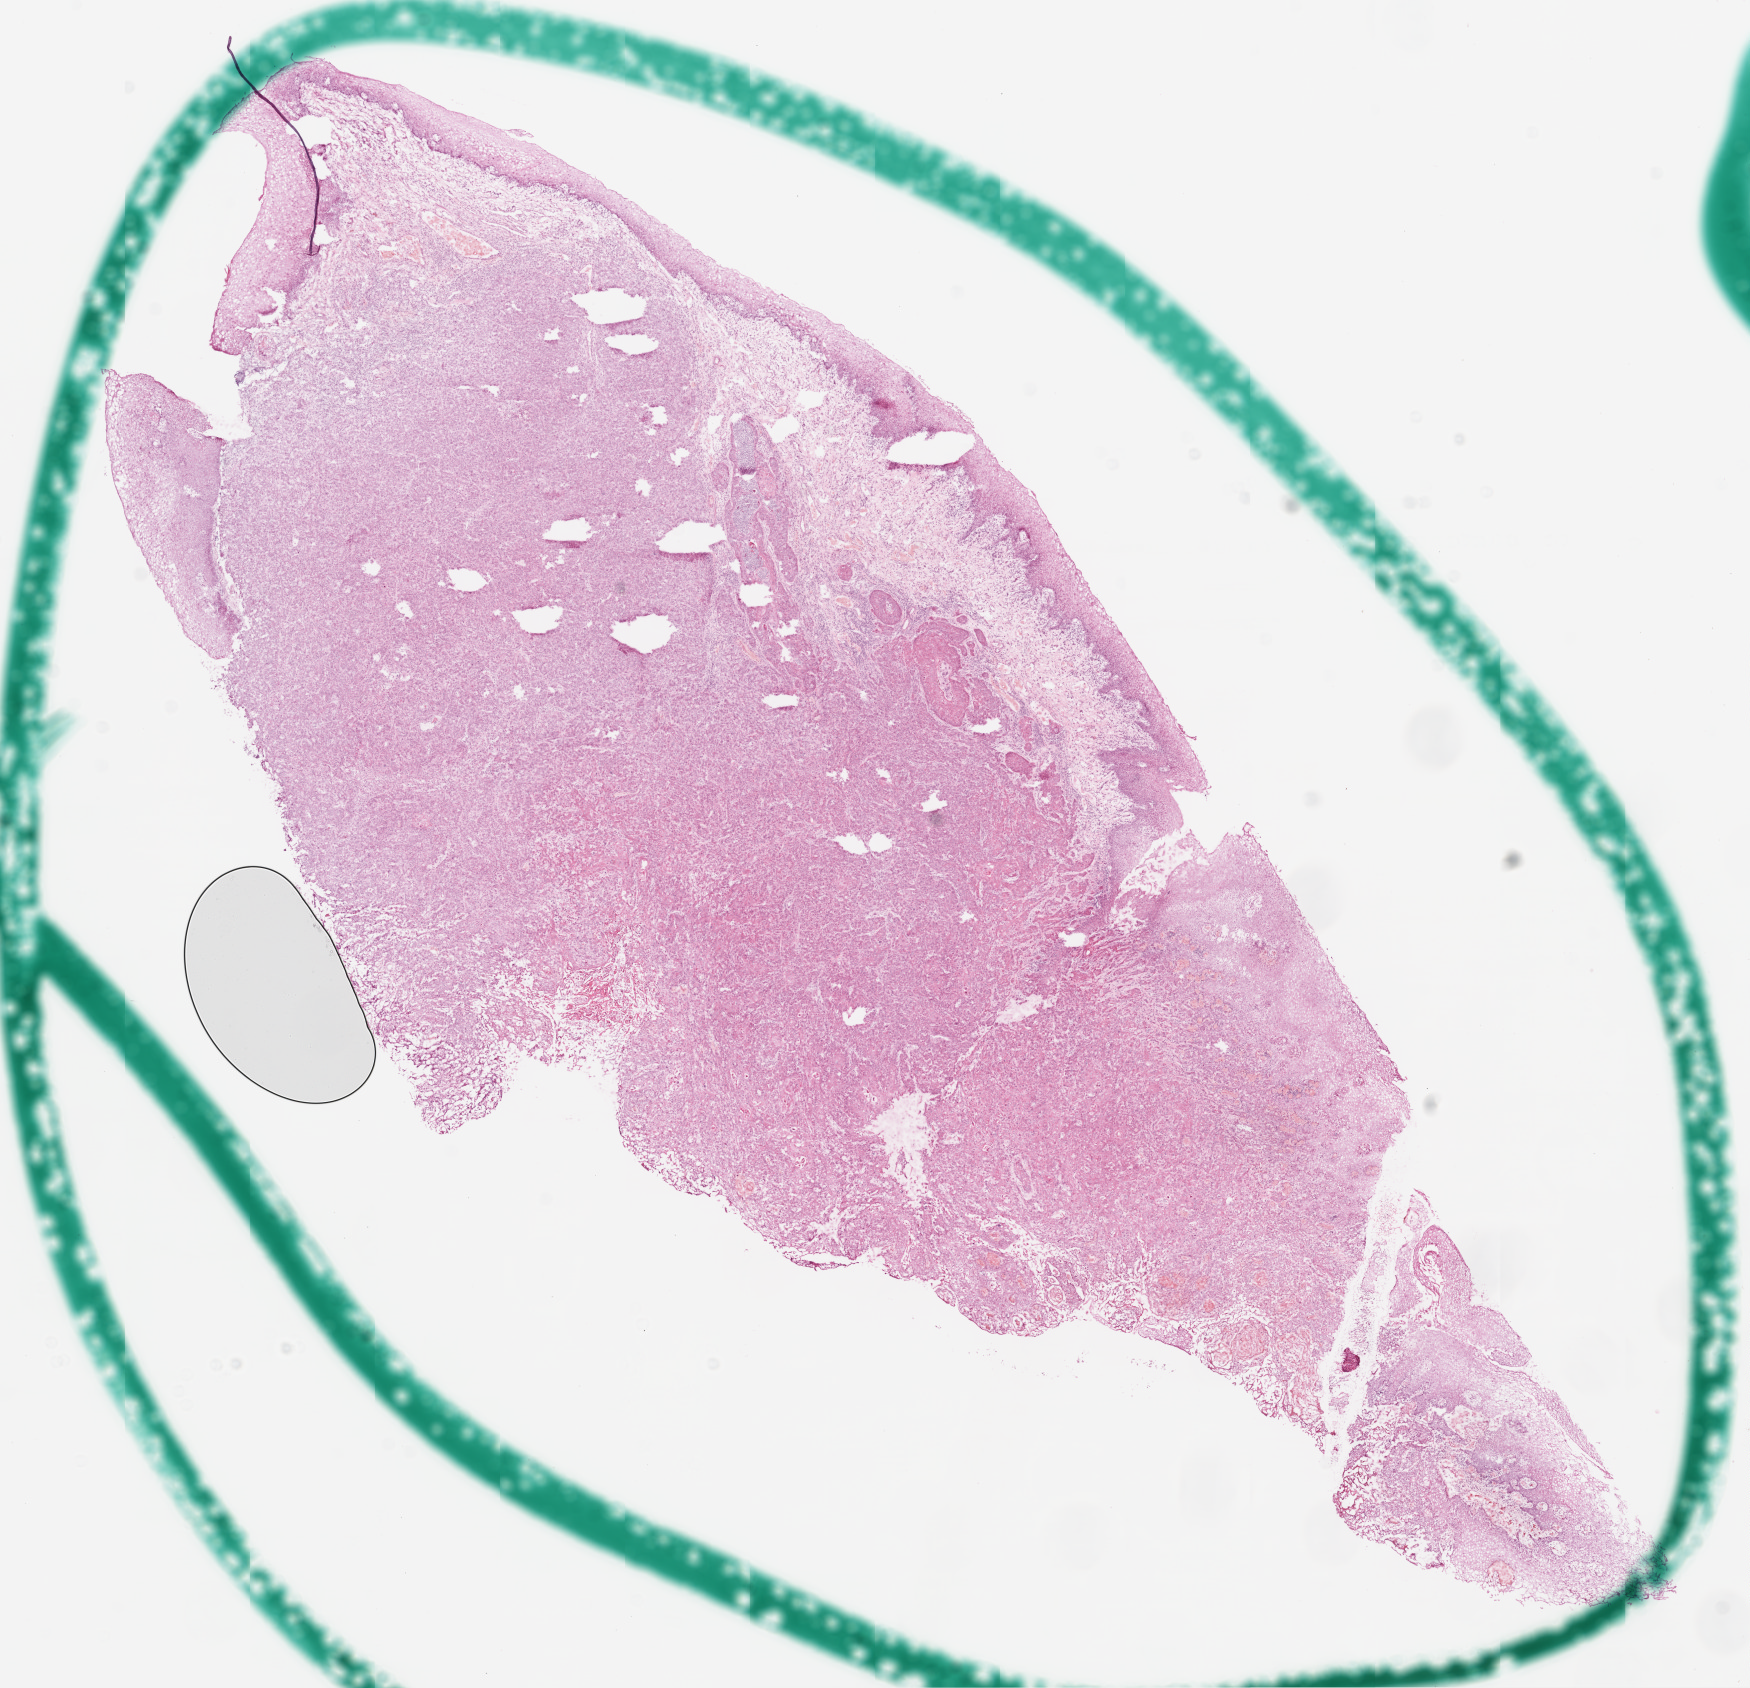
Whole-slide histology image, H&E — a low-resolution overview of the entire scanned area, about 14.0 x 13.5 mm (from a 20x scan), frozen section from the top of the tissue portion, head and neck, primary tumour sample. Male patient; age at initial diagnosis 66 years. Histologic grade: G2 (moderately differentiated). Slide review estimates, as recorded: tumour cells 86%, tumour nuclei 80%, normal cells 10%, stromal cells 4%, necrosis 0%. Infiltration values recorded for this section: lymphocyte infiltration 1%, neutrophil infiltration 10%.
• AJCC pathologic stage: IVA (7th edition)
• TNM: T4a N2b
• diagnosis: Squamous cell carcinoma, NOS (hypopharynx, NOS)